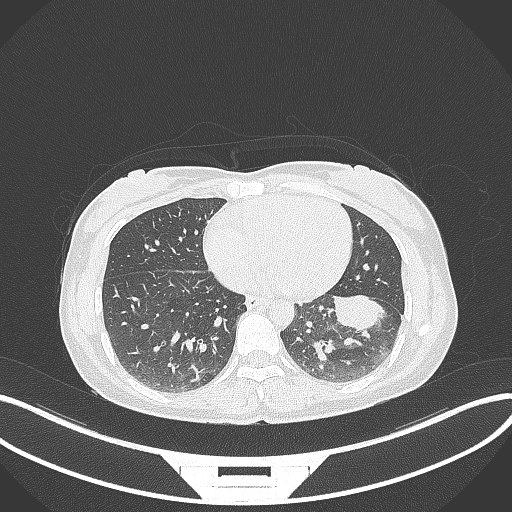
Chest CT, one axial slice. Position 17 of 244 along the scan axis. Reconstruction kernel B70f. Lung window (W 1500 / L -600 HU). 512 × 512 image matrix, field of view 400 × 400 mm. Patient: female, 41 years. From the clinical record (not read from this slice): clinical TNM (as recorded): T2a N3 M1b.
Outlined on this slice (bounding box drawn by a radiologist):
- lung tumour (recorded histology: adenocarcinoma): box from (x=333, y=291) to (x=394, y=332) px